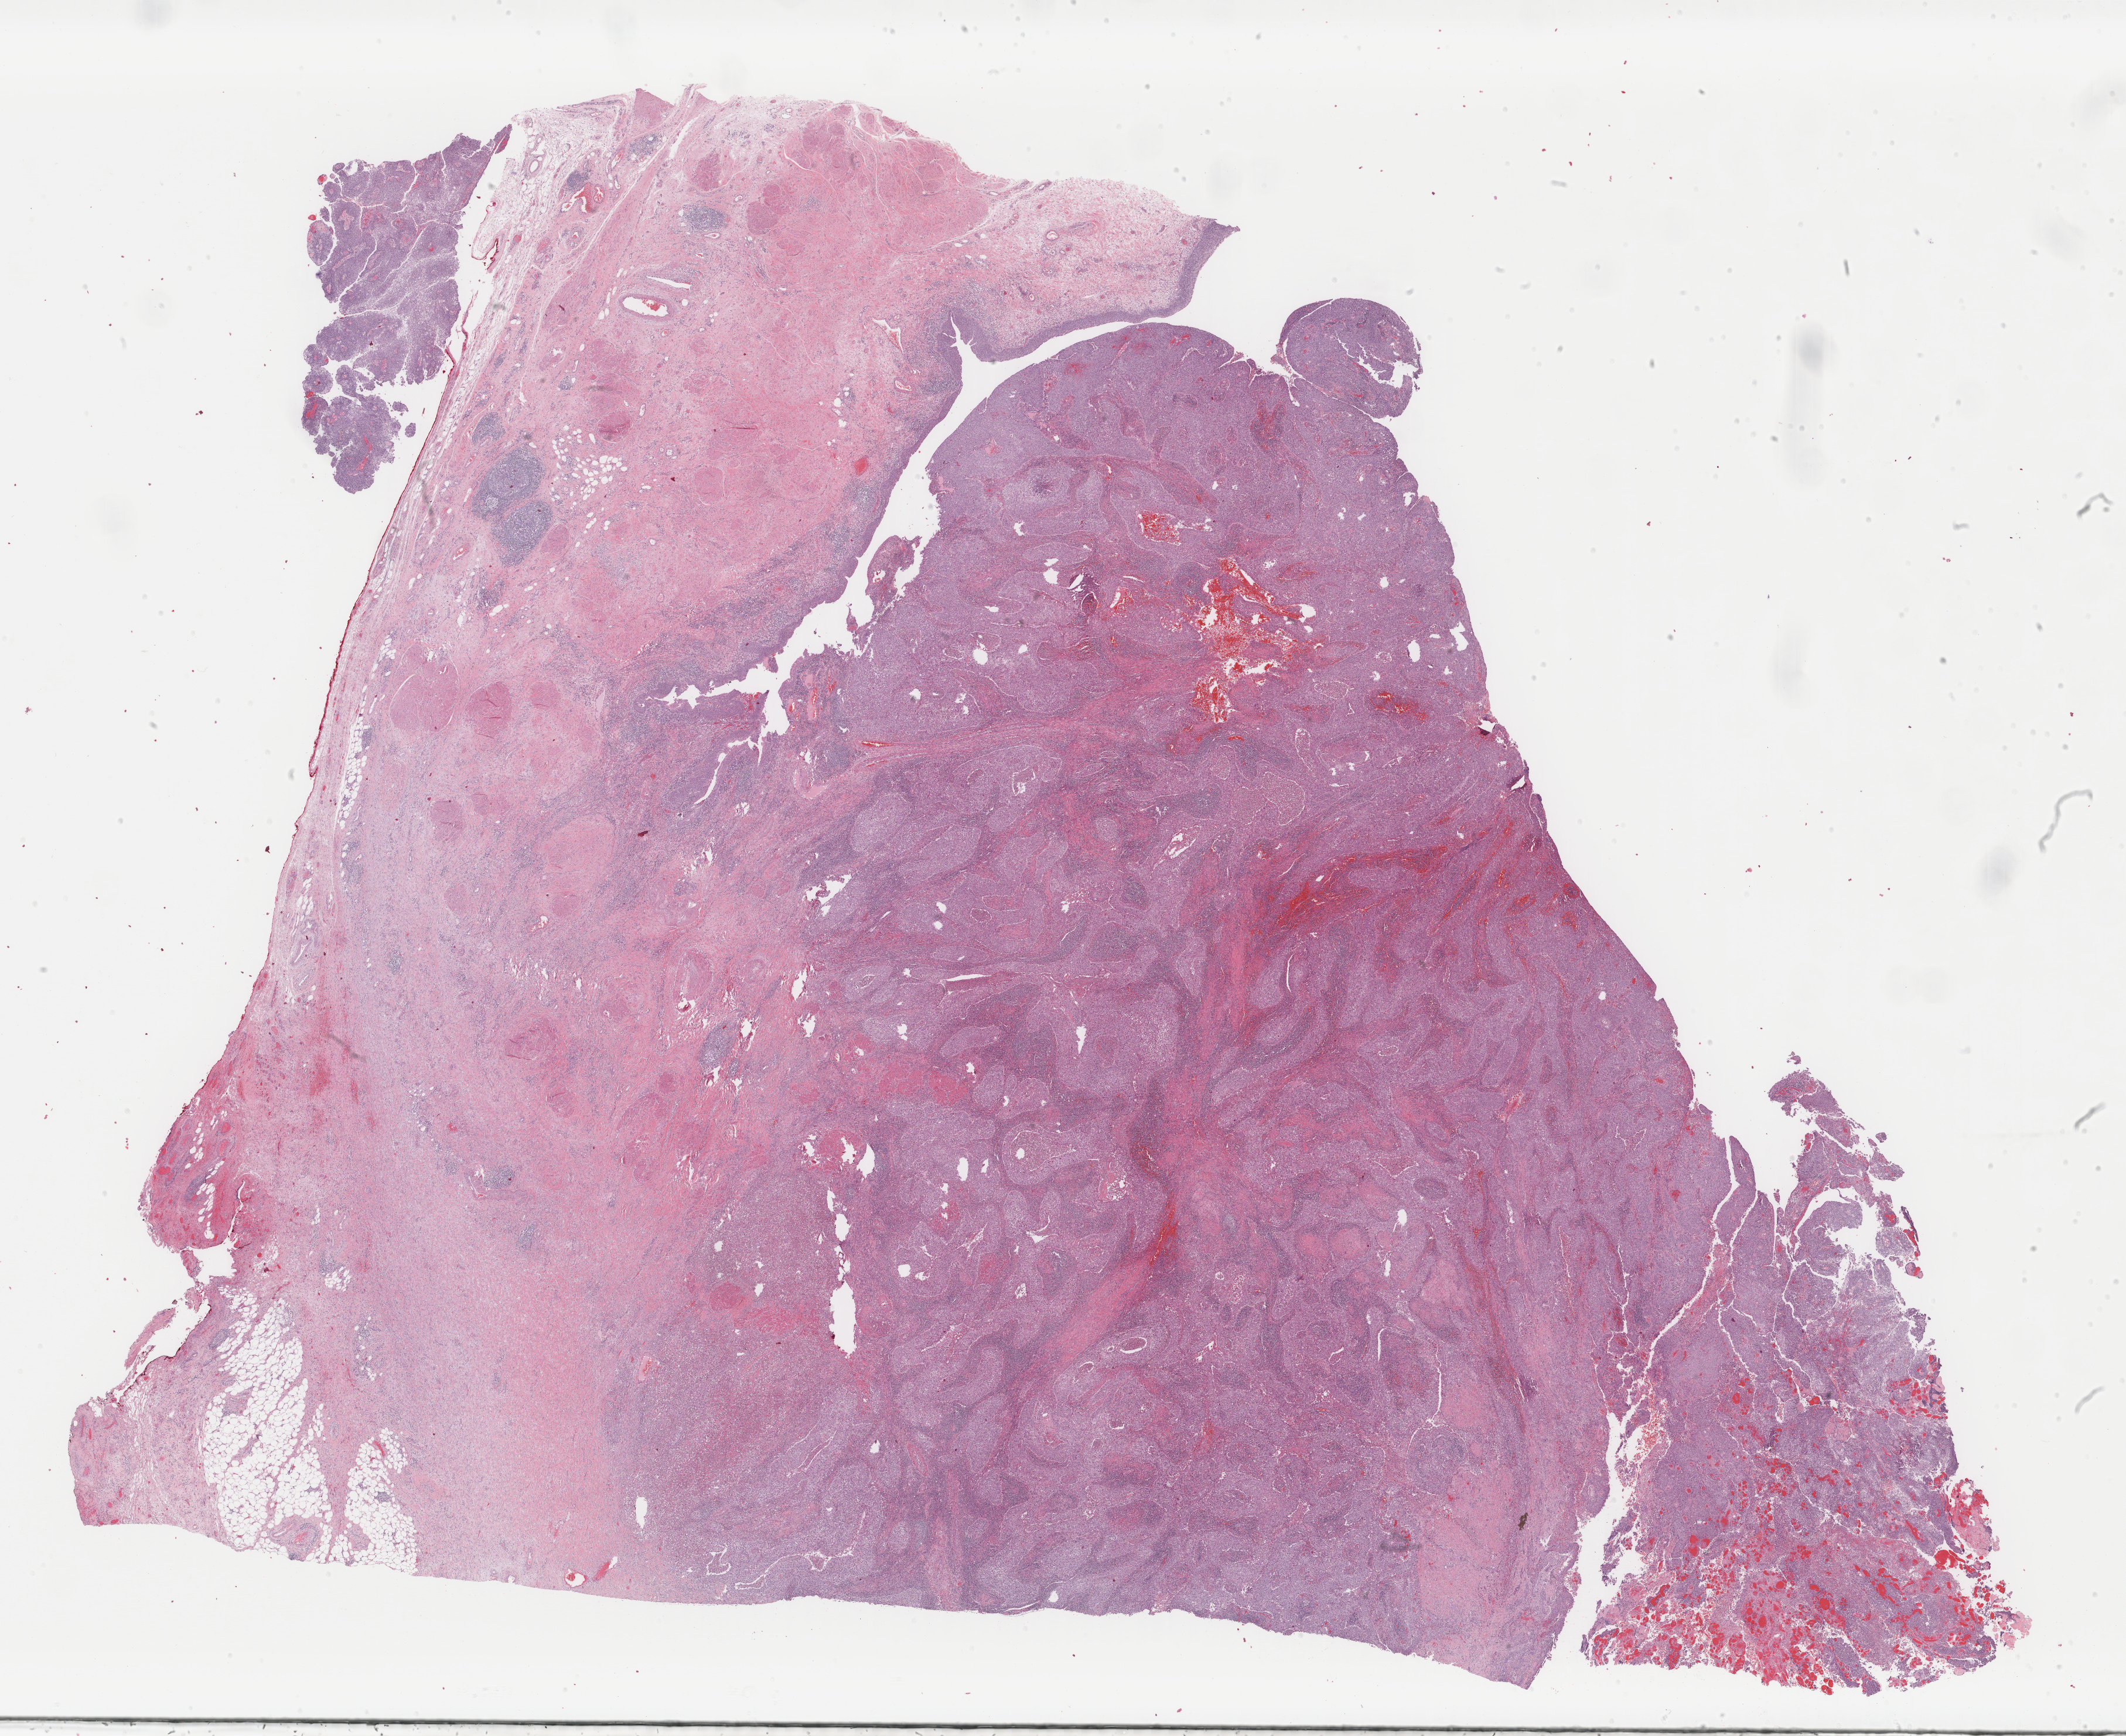
H&E-stained whole-slide image — whole scanned area (about 28.8 x 23.5 mm) shown as a low-resolution overview, formalin-fixed paraffin-embedded (FFPE) diagnostic section, sample: primary tumour, bladder. Male, age 80 years at initial diagnosis. Histologic grade: high grade.
Diagnosis: Transitional cell carcinoma (posterior wall of bladder). AJCC pathologic stage: II. Lymph nodes positive (case pathology): 0 of 3 examined.